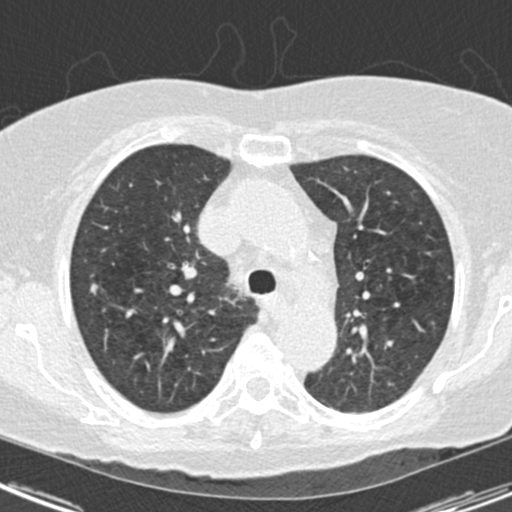
Low-dose screening chest CT, one axial slice. Position 117 of 163 along the scan axis. Reconstruction kernel B30f. 120 kVp. Lung window (W 1500 / L -600 HU). 2 mm slice thickness. 512 × 512 image matrix.
Annotated regions visible in this slice (manually delineated by an expert):
- lesion 1 (tumor, upper lobe of right lung): bounding box (x1, y1, x2, y2) in pixels: (90, 283, 98, 292)